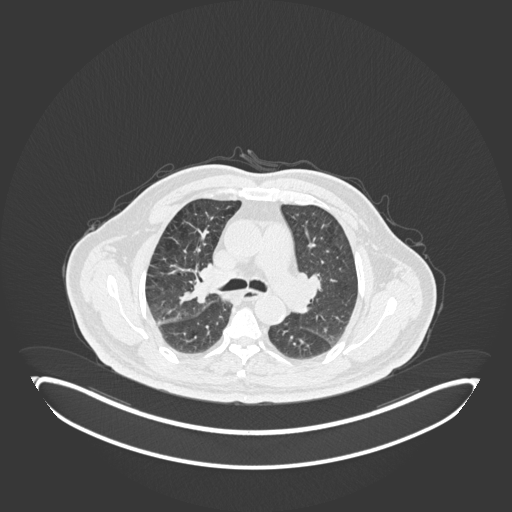
Chest CT, one axial slice; reconstruction kernel B30f; 120 kVp; lung window (W 1500 / L -600 HU); 1 mm slice thickness; 512 × 512 image matrix, field of view 500 × 500 mm. Male patient, age 72 years. Case-level facts recorded for this patient, not image findings: clinical TNM (as recorded): T1c N0 M0.
Structures marked on this image (rectangle marked by the reading radiologist):
- lung tumour (recorded histology: squamous cell carcinoma): box from (x=185, y=262) to (x=212, y=305) px